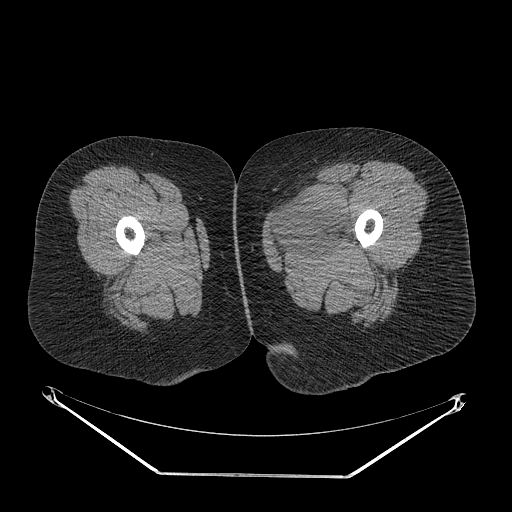
CT of an extremity soft-tissue mass (from a PET/CT study), one axial slice. Position 18 of 267 along the scan axis. Reconstruction kernel STANDARD. 140 kVp. Soft-tissue window (W 400 / L 40 HU). 3.75 mm slice thickness. 512 × 512 image matrix, field of view 500 × 500 mm. Female patient. From the clinical record (not read from this slice): histological type: myxofibrosarcoma; grade: intermediate; site of the primary tumour: left thigh.
Outlined on this slice (expert contour drawn on MRI and transferred to this co-registered scan by the dataset authors):
- gross tumour volume including surrounding oedema: bounding box (x1, y1, x2, y2) in pixels: (274, 190, 350, 254)
- gross tumour volume (mass): (278, 194, 346, 254)